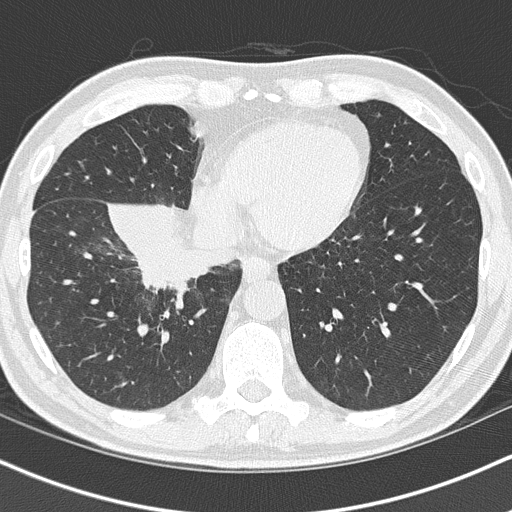
Low-dose screening chest CT, one axial slice; position 38 of 151 along the scan axis; reconstruction kernel B50f; 120 kVp; lung window (W 1500 / L -600 HU); 2 mm slice thickness; 512 × 512 image matrix, field of view 320 × 320 mm.
Outlined on this slice (expert manual segmentation):
- lesion 1 (tumor, hilum of right lung): box from (x=139, y=234) to (x=209, y=285) px